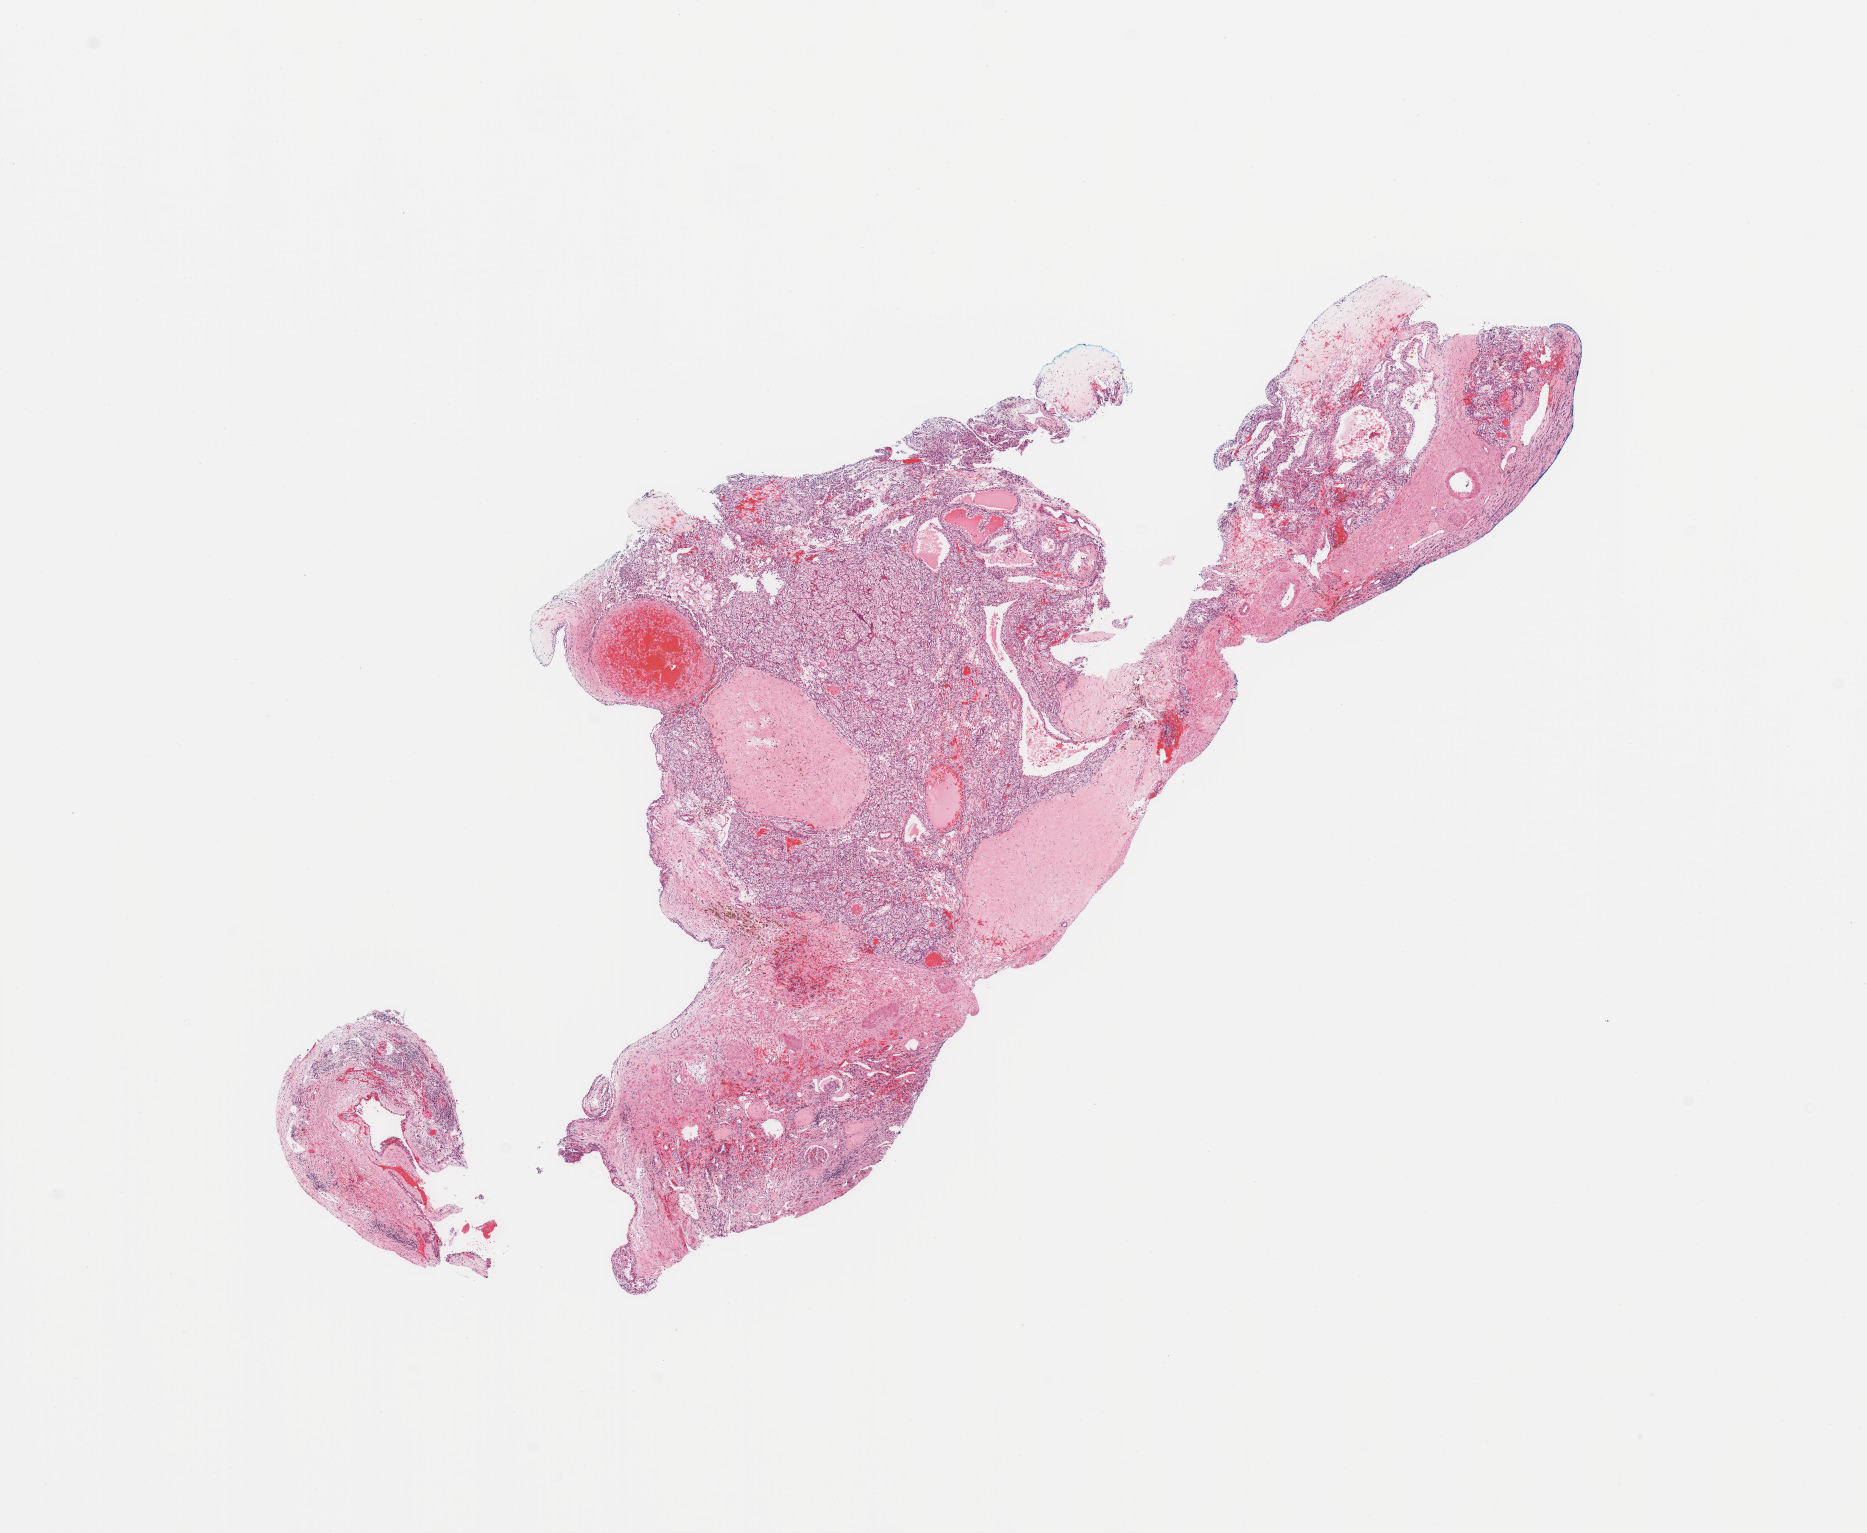
Whole-slide histology image, H&E-stained — low-resolution overview of the scanned area, about 14.8 x 12.1 mm (acquisition: 20x scan); tumour tissue sample, sampled site: kidney. Male, 56 y/o. Histologic grade: G2 (moderately differentiated). Slide review estimates, as recorded: tumour nuclei 80%, necrosis 7%.
- diagnosis: Renal cell carcinoma, NOS
- AJCC pathologic stage: I